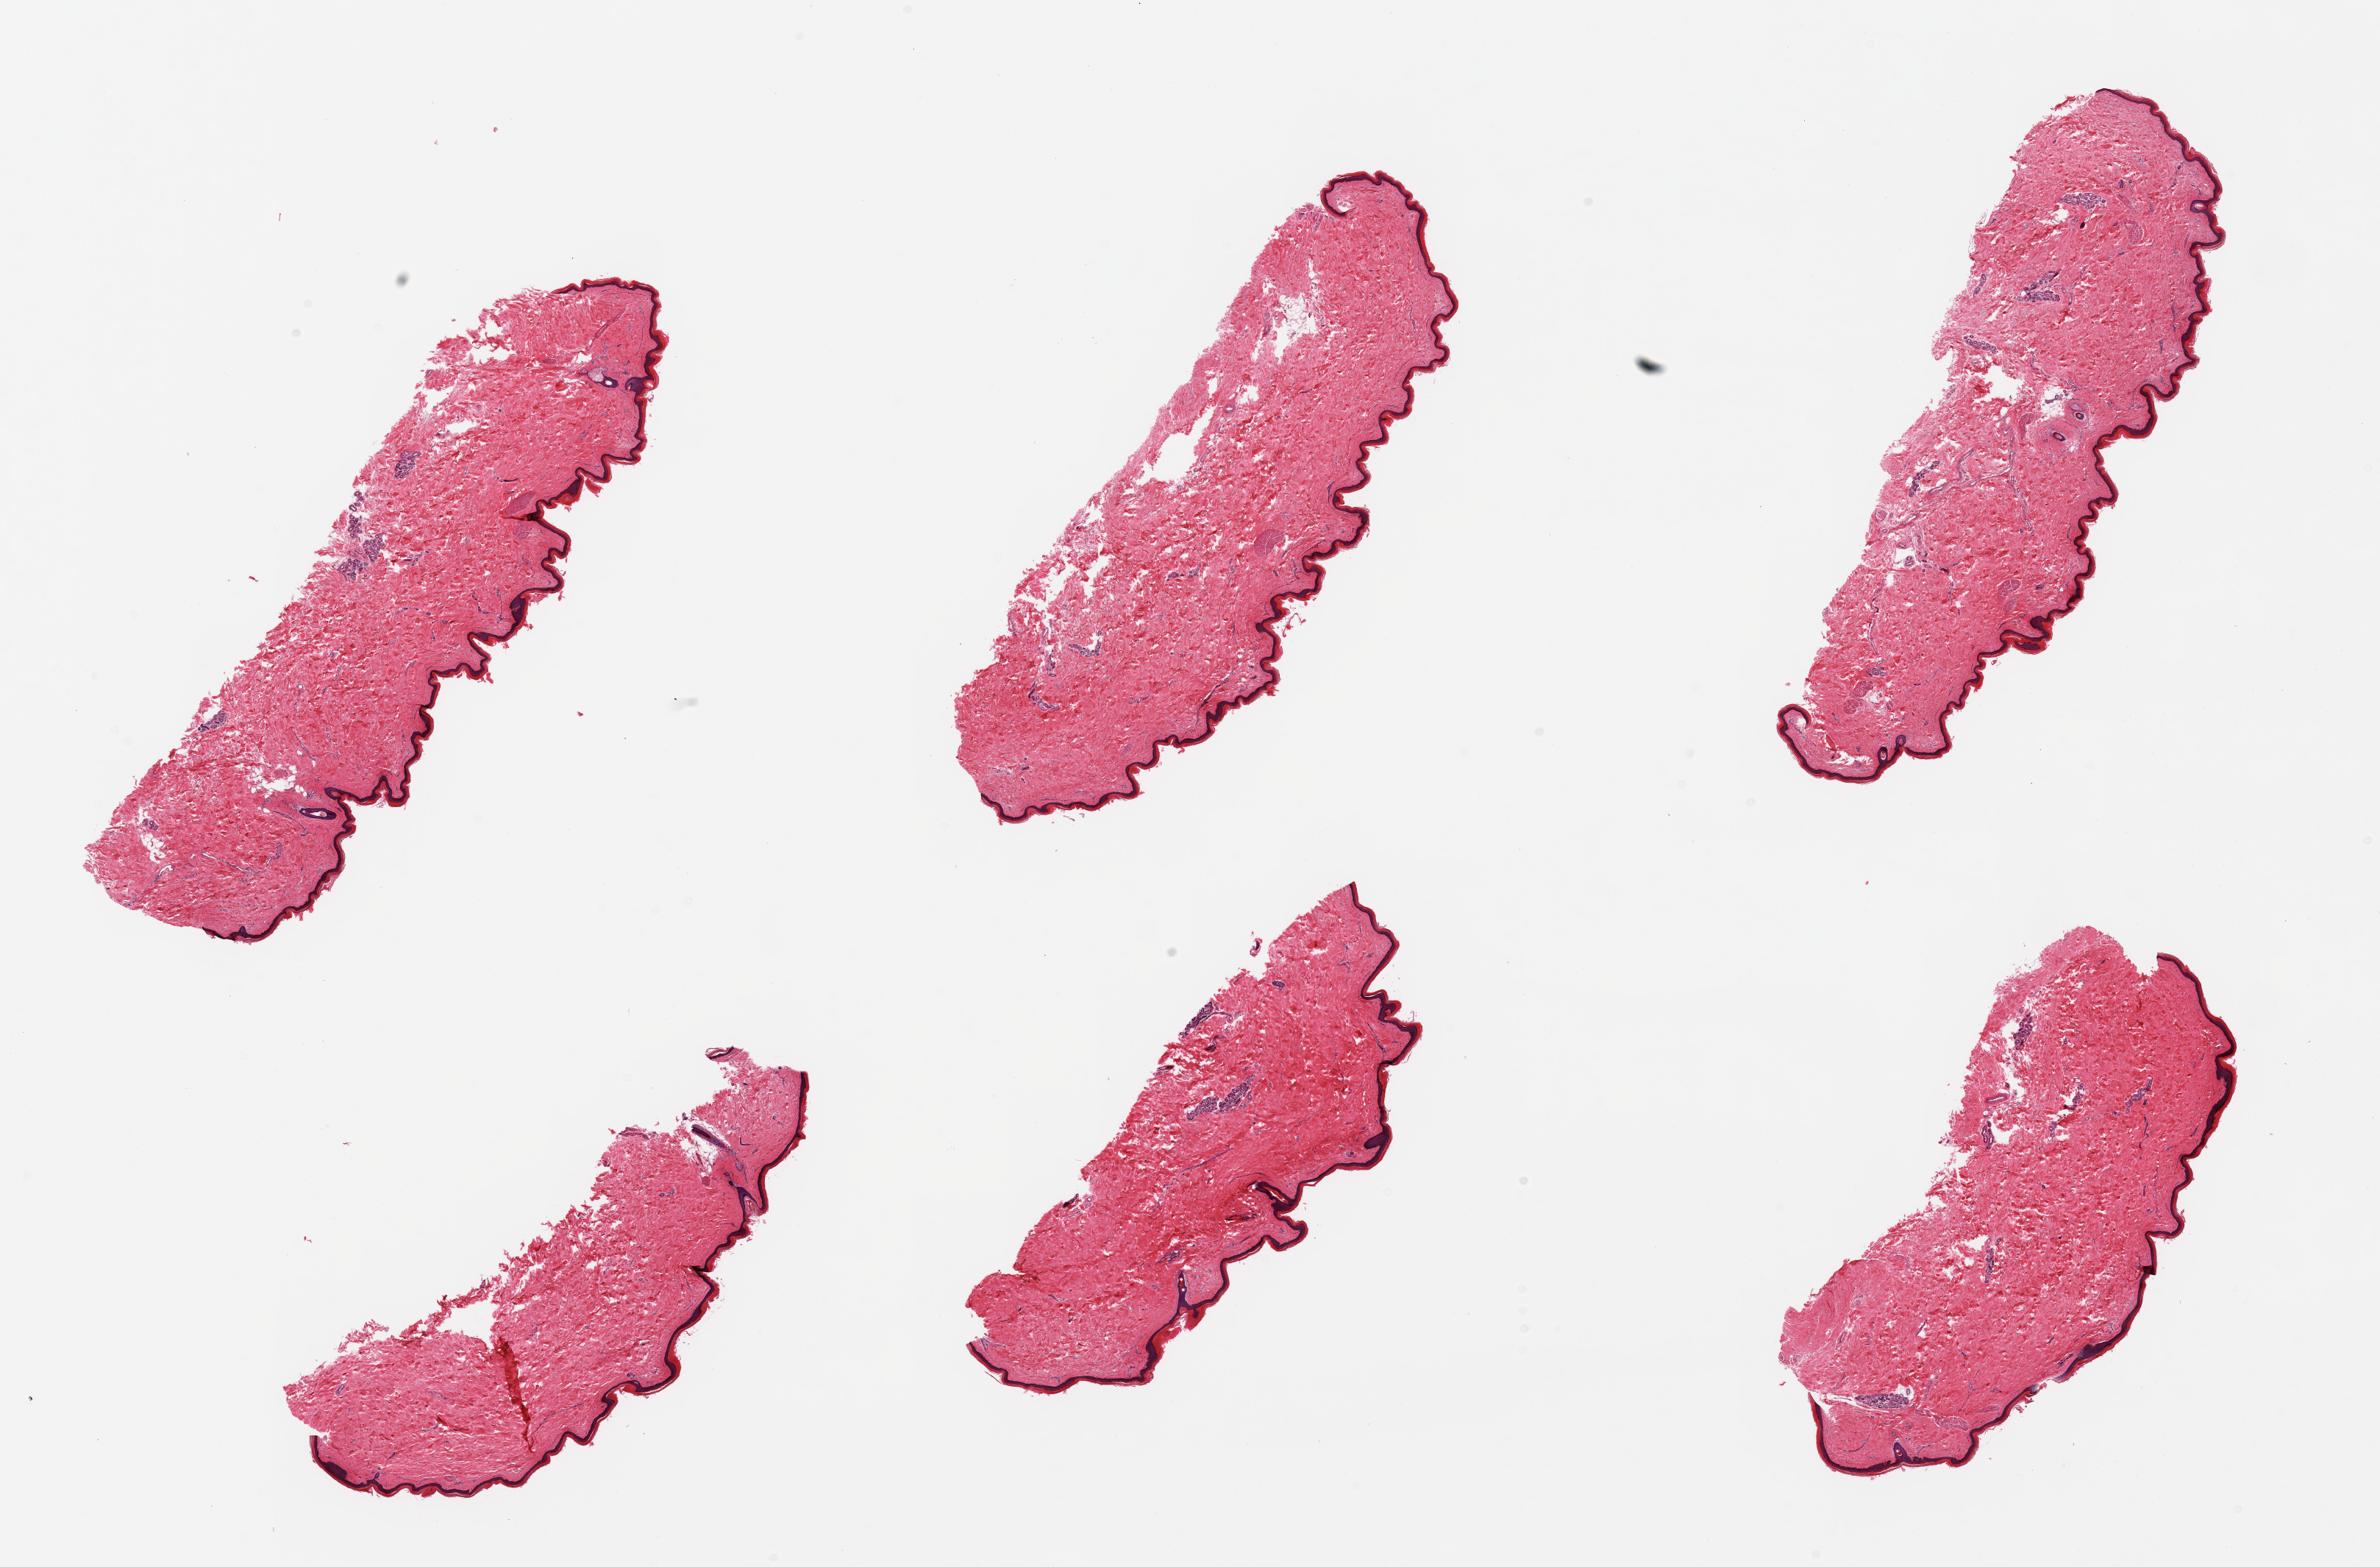
Whole-slide image, haematoxylin and eosin stain, shown as a low-resolution overview of the whole scanned area (about 25.6 x 16.8 mm), PAXgene-fixed paraffin-embedded (PFPE) section, target tissue: skin of lower leg, donor tissue sample. Female donor.
Review note (as recorded): 6 pieces; well trimmed.